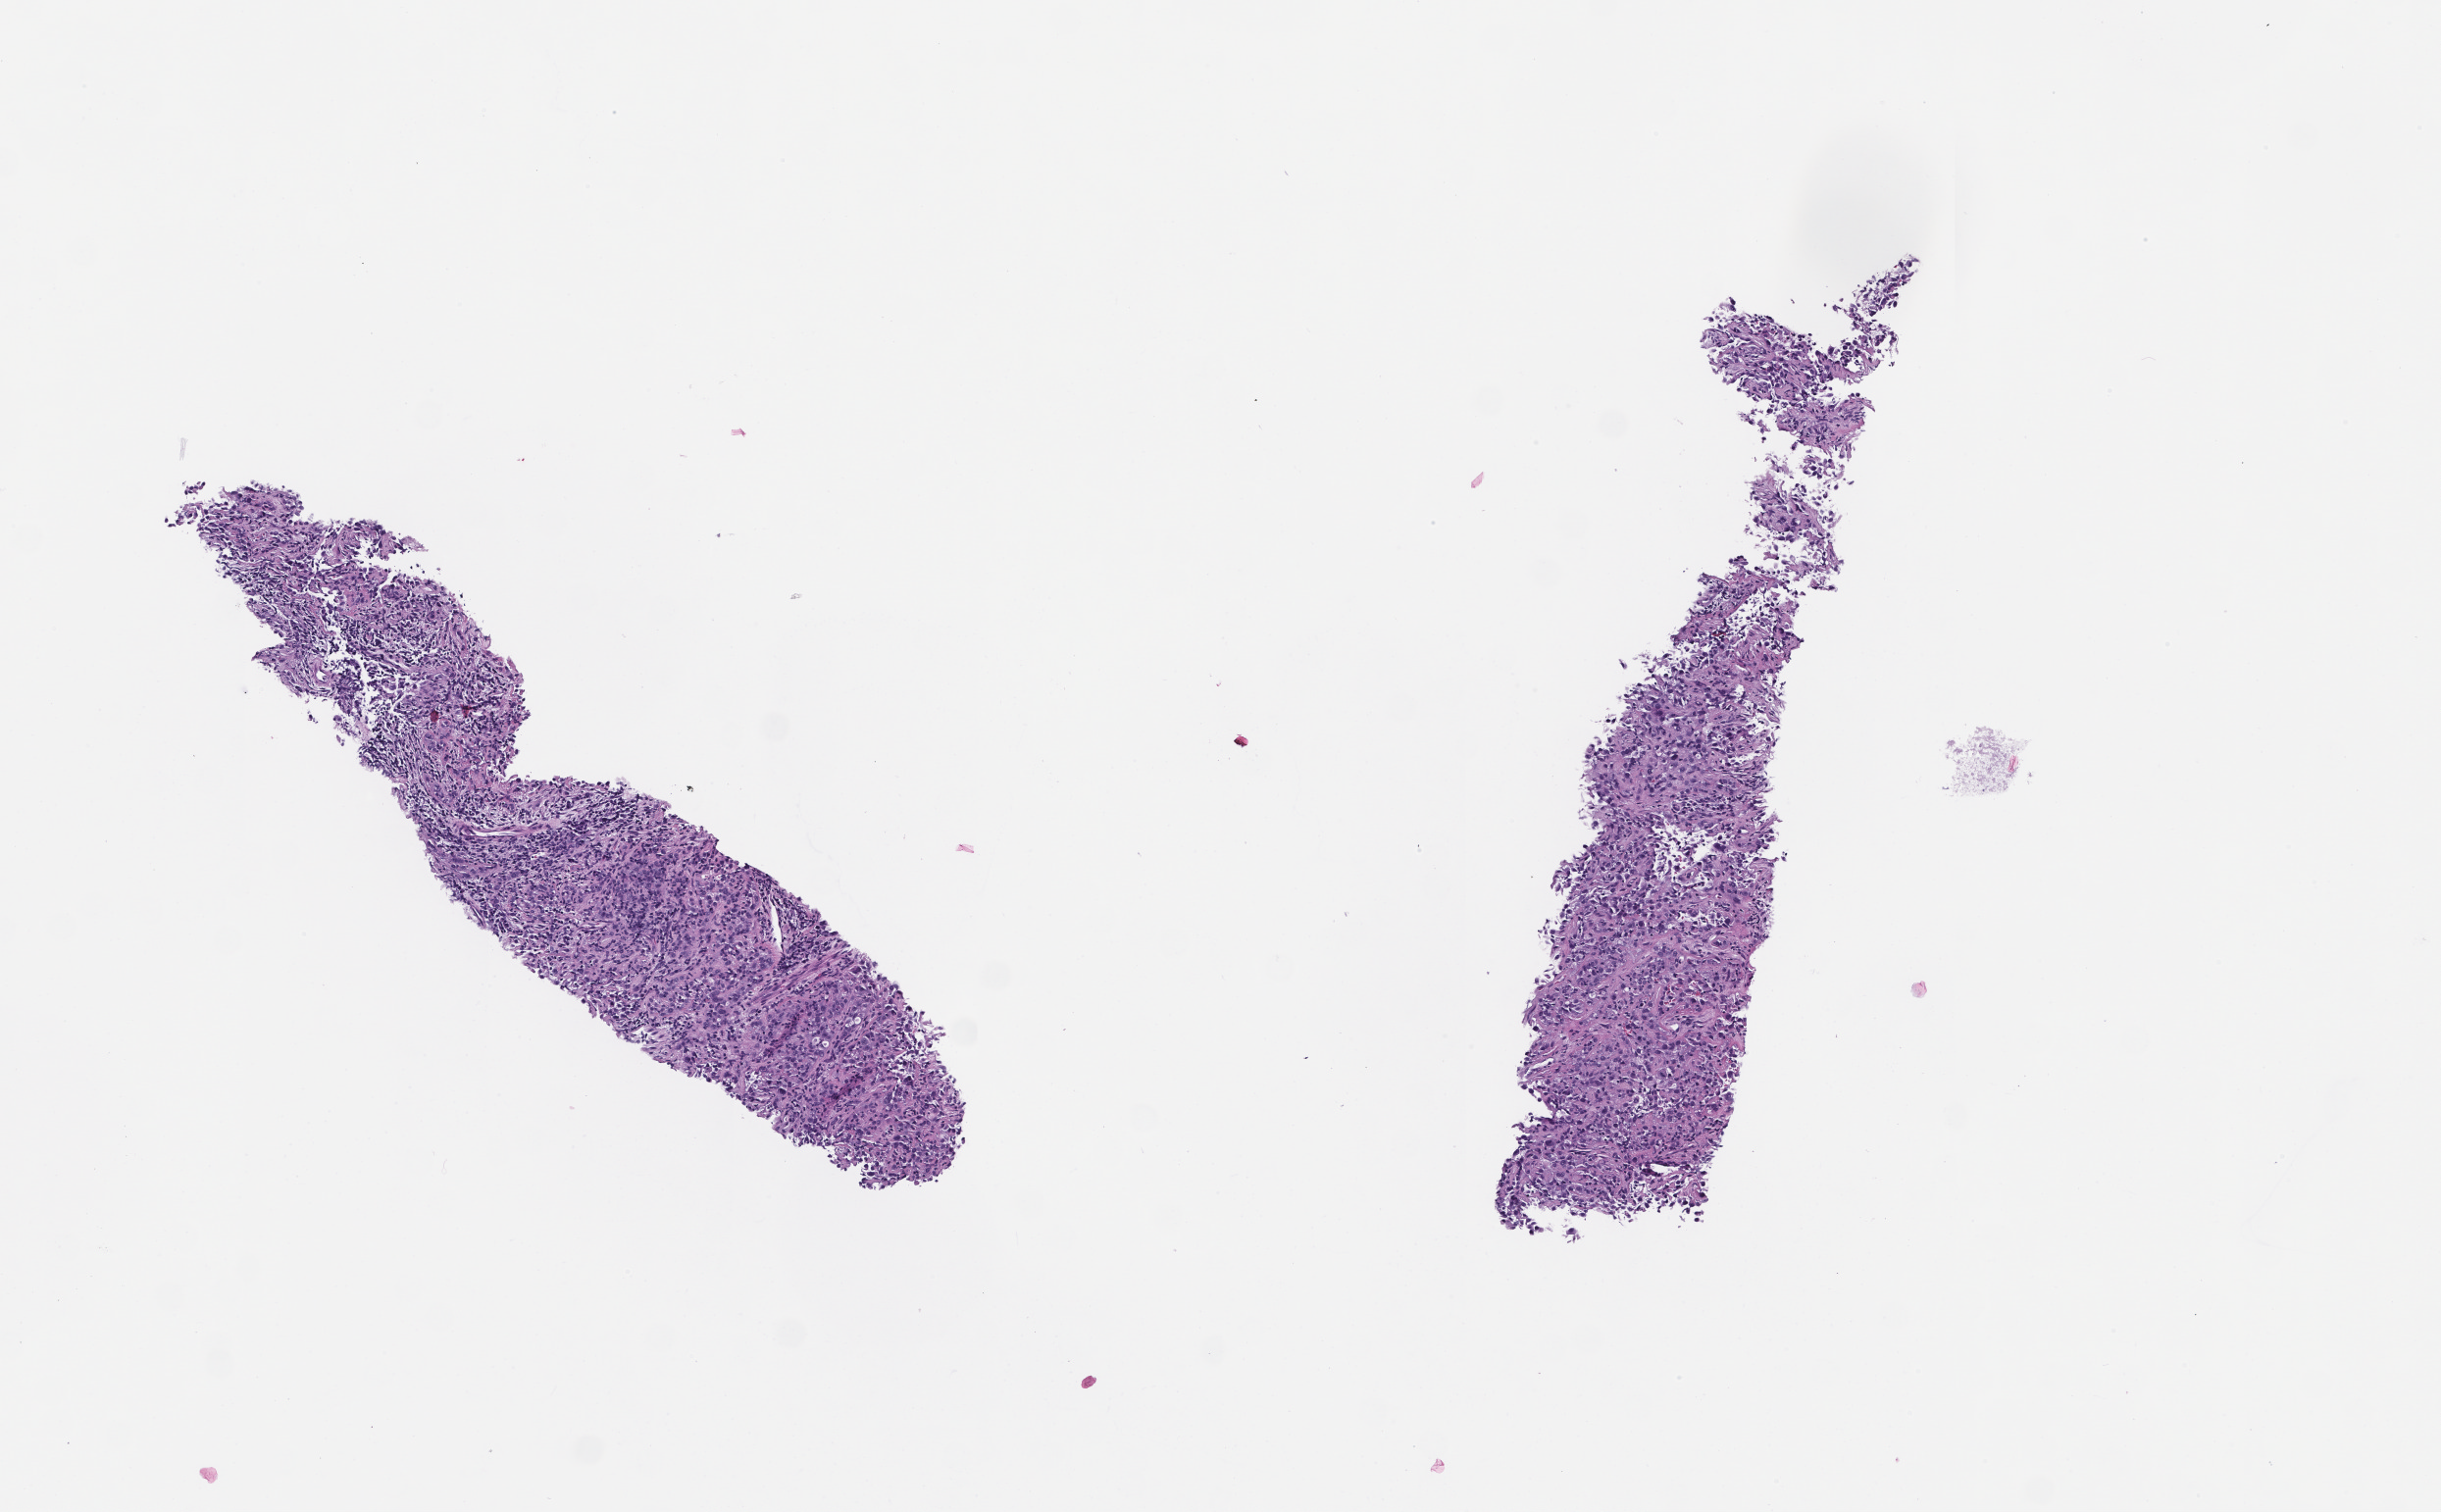
Digitized H&E-stained section — shown as a low-resolution overview of the whole scanned area (about 5.0 x 3.1 mm). FFPE section. Tissue site: lung. Specimen time point: collected at baseline (before treatment). Patient sex: male.
- this section: primary tumour tissue
- diagnosis: Non-Small Cell Lung Carcinoma